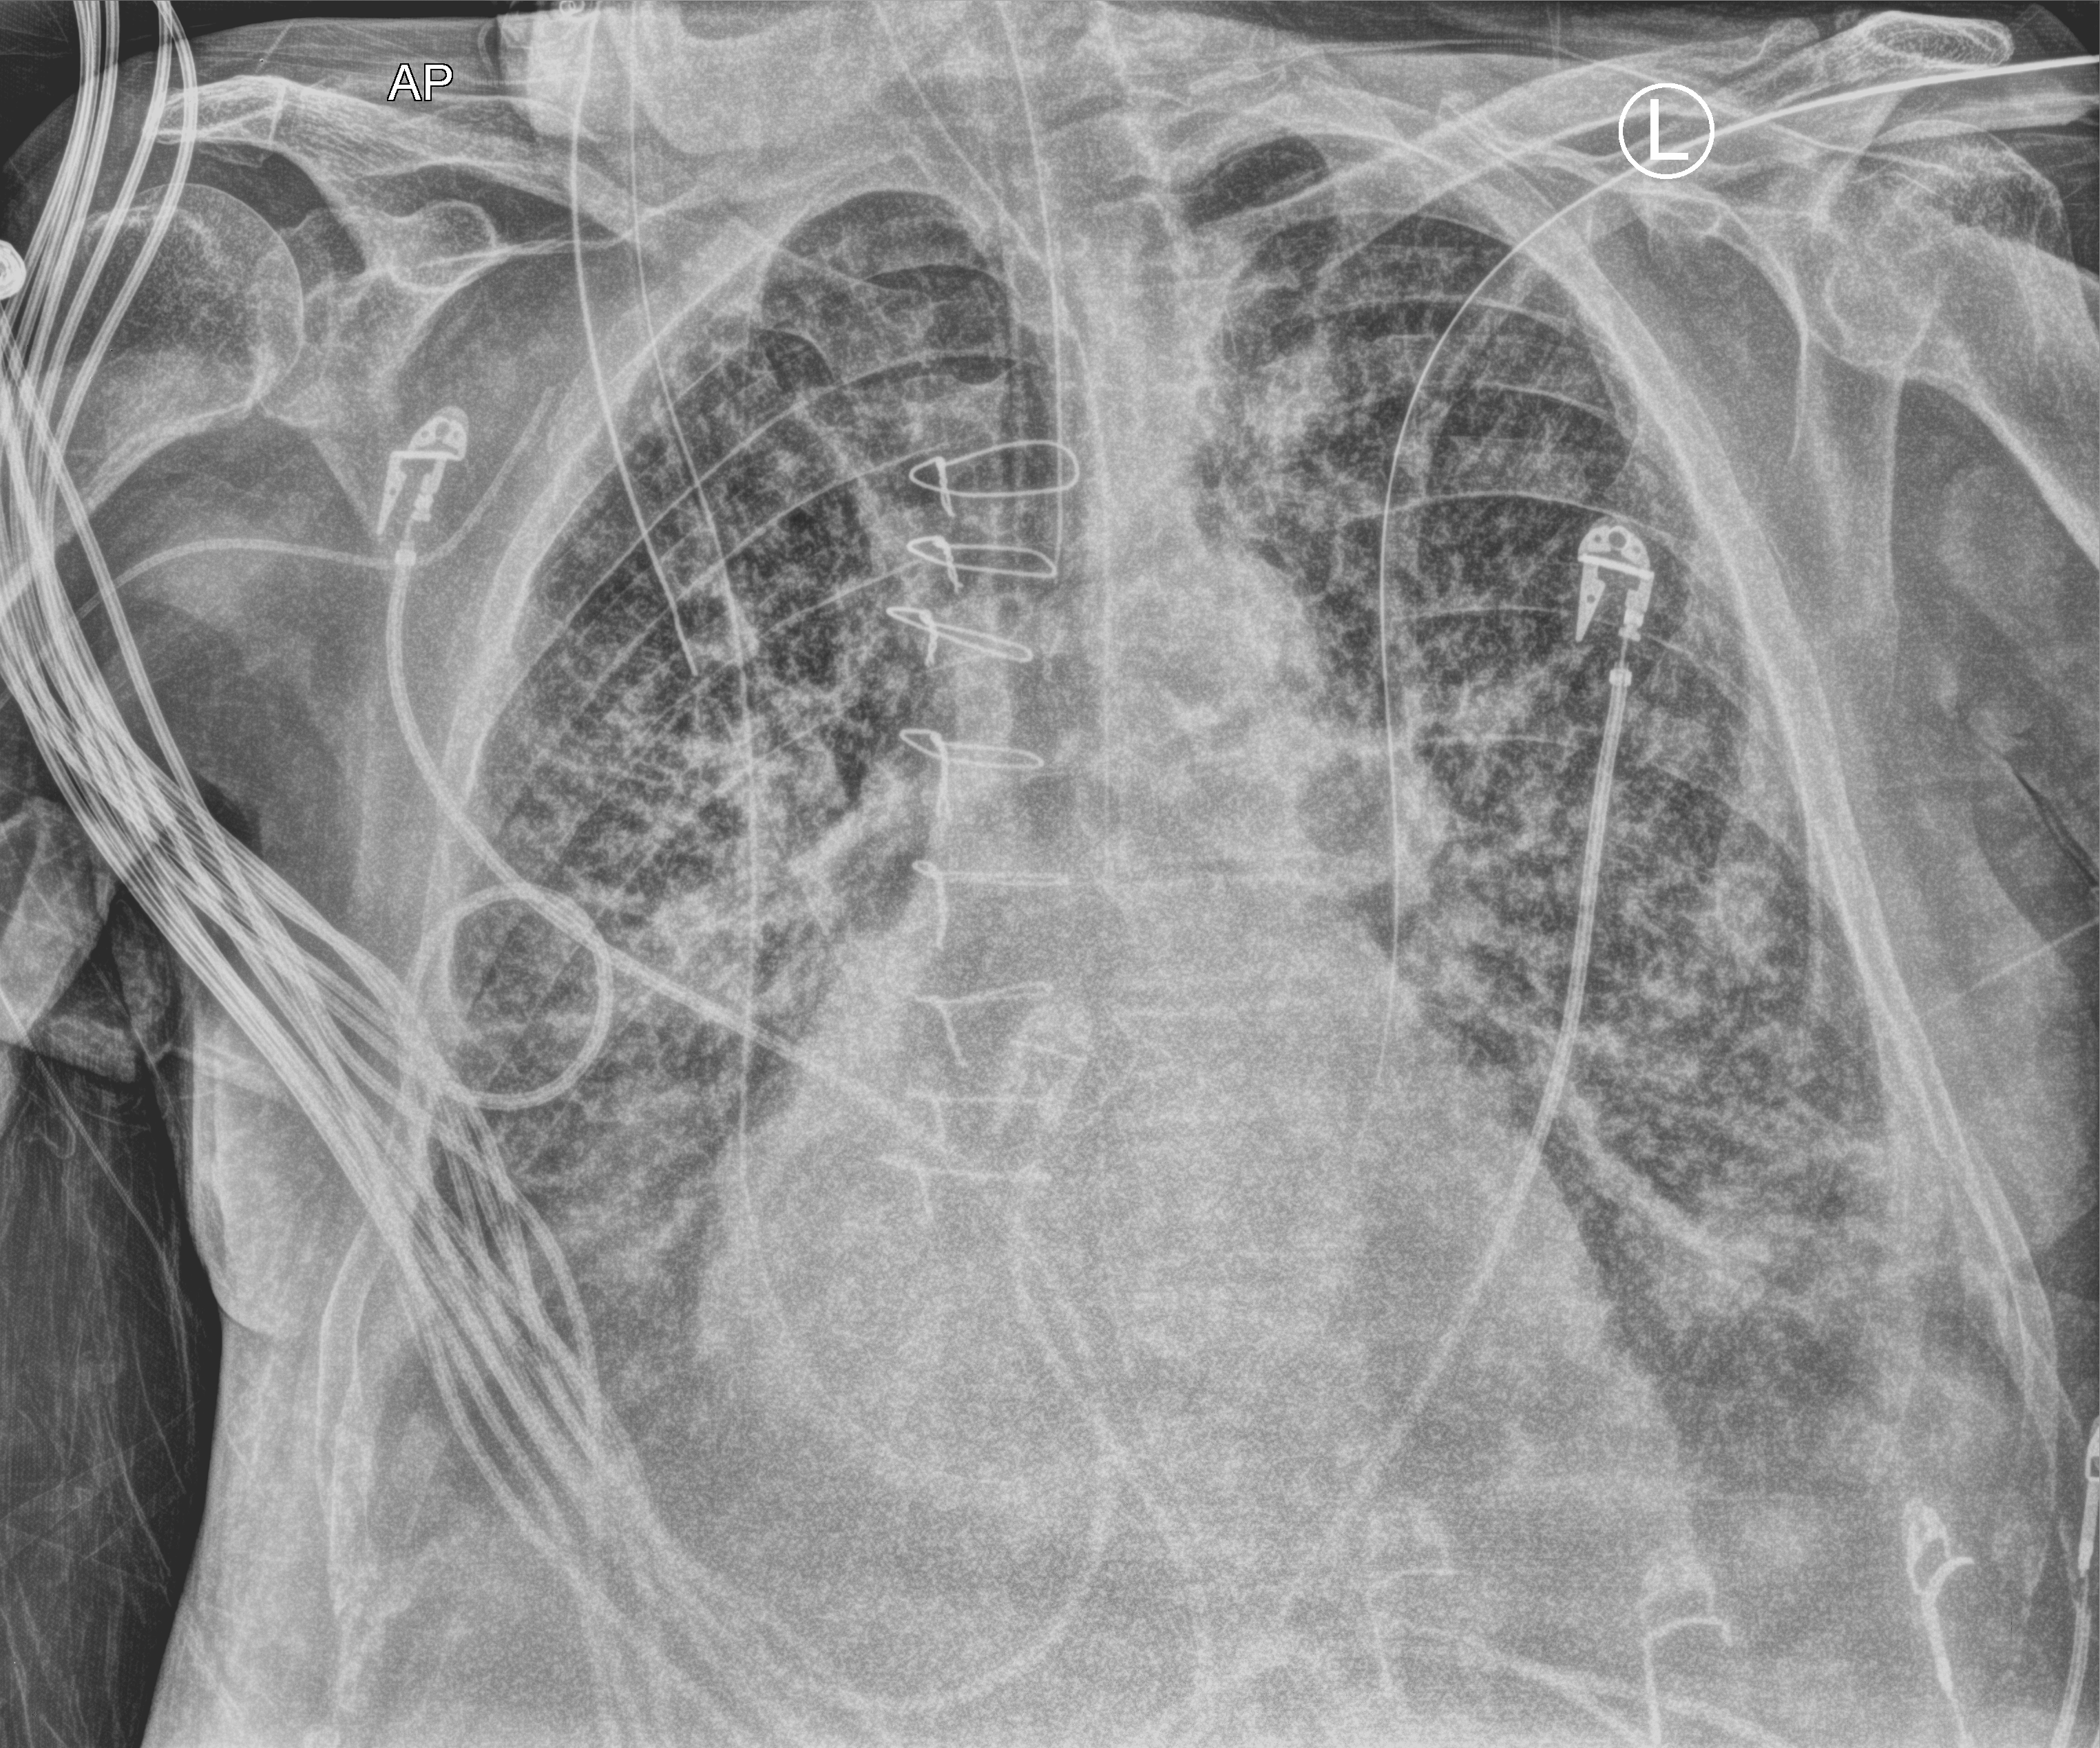
Chest X-ray (portable); anteroposterior (AP) projection. Male patient hospitalised with COVID-19, age 75–90 years.
Hospital-stay facts (about this admission, not read from this image; timing relative to this image not recorded):
- admitted to intensive care during this hospital stay: yes
- mechanically ventilated during this hospital stay: yes